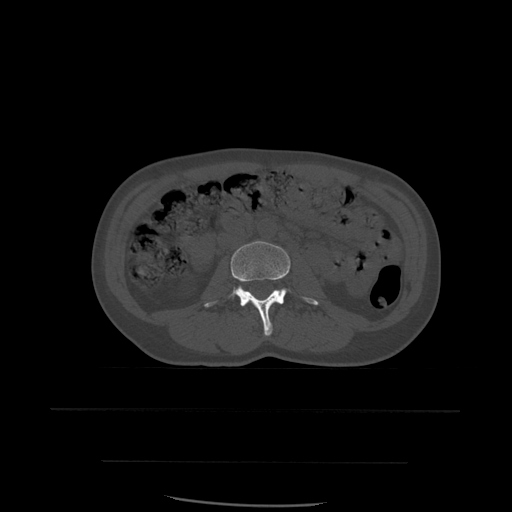
CT including the spine, one axial slice; slice 197 of 574 in the series (ordered by position); bone window (W 1800 / L 400 HU); 1.25 mm slice thickness; 512 × 512 image matrix, field of view 392 × 392 mm. Patient age 48 years. From the clinical record (not read from this slice): primary cancer: lung; vertebrae with lytic lesions (as recorded): T11.
Outlined on this slice (semi-automatically segmented with operator editing):
- L3 vertebra: bounding box (x1, y1, x2, y2) in pixels: (204, 241, 319, 337)